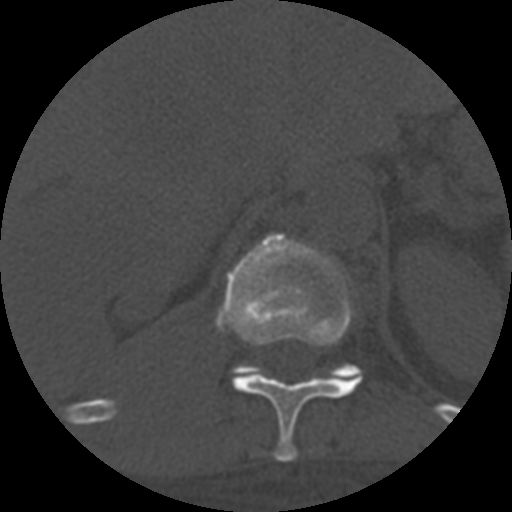
CT including the spine, one axial slice. Position 329 of 708 along the scan axis. Reconstruction kernel STANDARD. 120 kVp. One of 3 acquisitions stored at this slice position. Bone window (W 1800 / L 400 HU). 512 × 512 image matrix, field of view 160 × 160 mm. Patient age 55 years. Case-level facts recorded for this patient, not image findings: primary cancer: colon; vertebrae with lytic lesions (as recorded): T12, L1, L5.
Annotated regions visible in this slice (semi-automatic segmentation, software-assisted and operator-edited):
- T11 vertebra: bounding box [x1, y1, x2, y2] px = [217, 233, 362, 462]
- T12 vertebra: [236, 364, 363, 380]